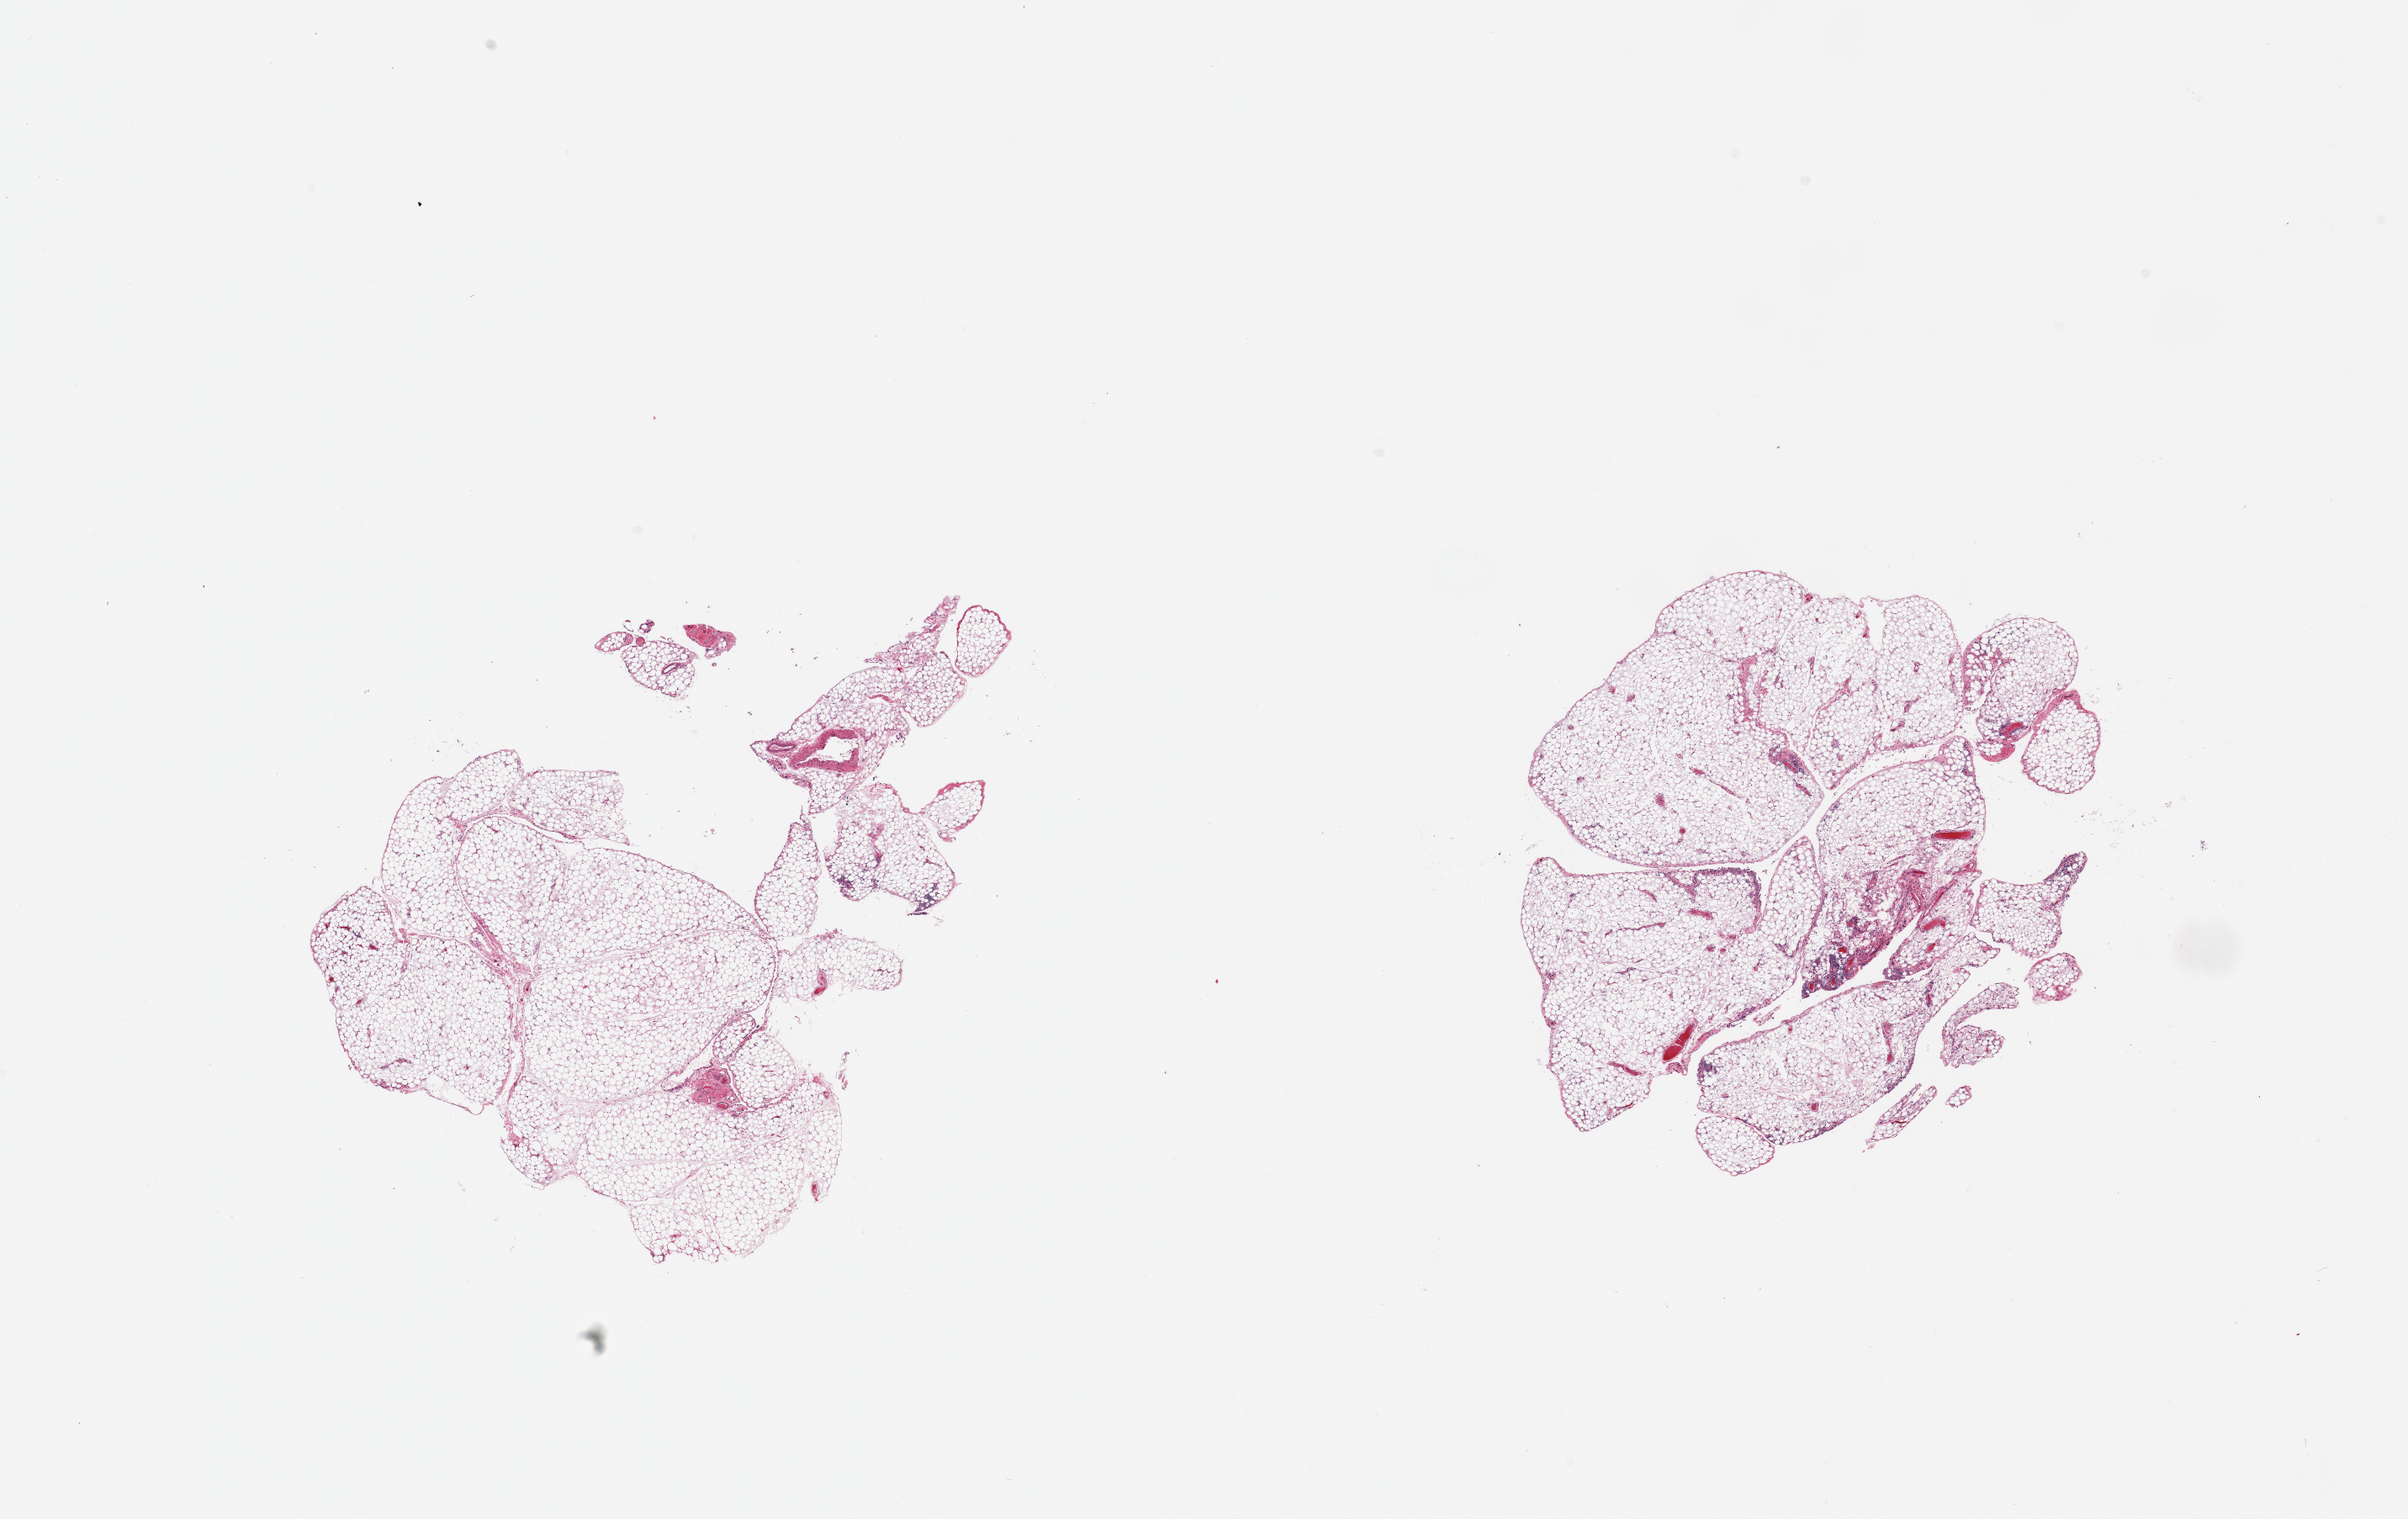
Whole-slide image, hematoxylin and eosin (H&E) stain — low-resolution overview of the scanned area, about 22.6 x 14.3 mm (acquisition: 20x scan). PAXgene-fixed paraffin-embedded (PFPE) section. Target tissue: omentum. Tissue donor sample. Donor: male.
• review note (as recorded): 2 pieces; lobulated mature adipose tissue and septal vessels; focal mesothelial lining cells and chronic inflammatory infiltrate